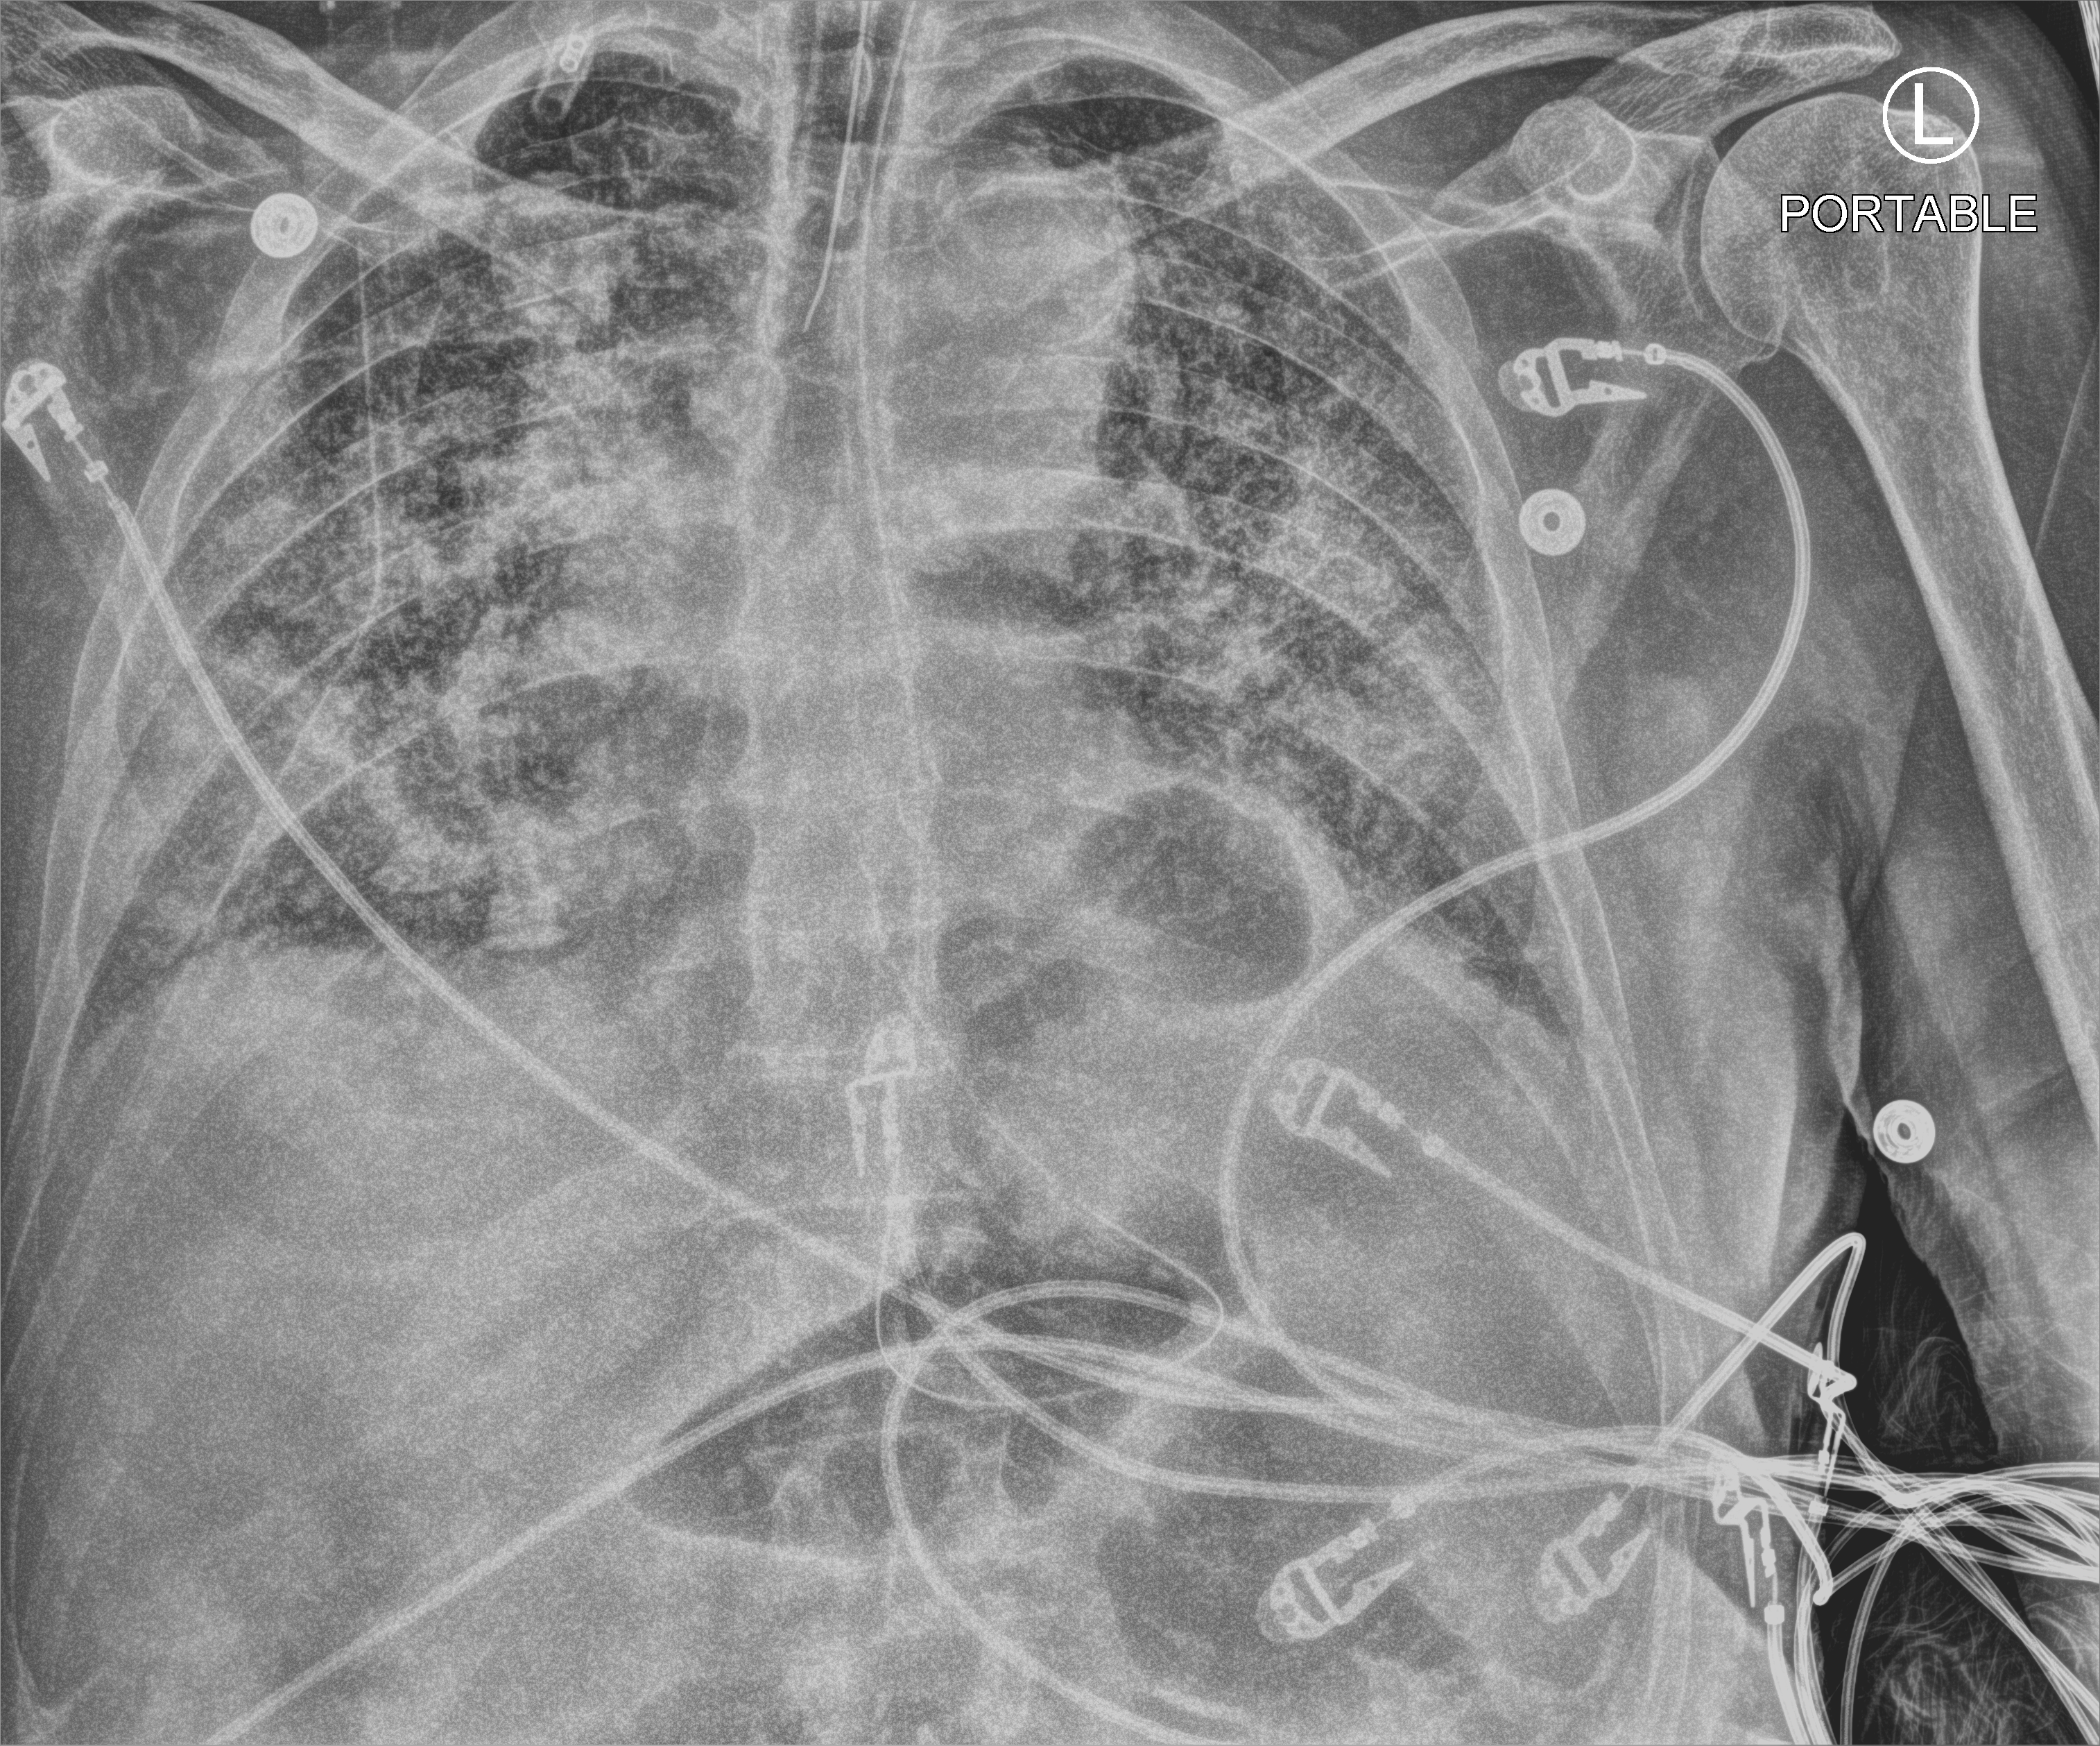
Chest X-ray (portable); anteroposterior (AP) projection. Patient hospitalised with COVID-19; male, aged 75–90 years.
From the hospital-stay record, not from the radiograph (when in the stay this image was taken is not recorded):
- length of hospital stay: 10 days
- admitted to intensive care during this hospital stay: yes